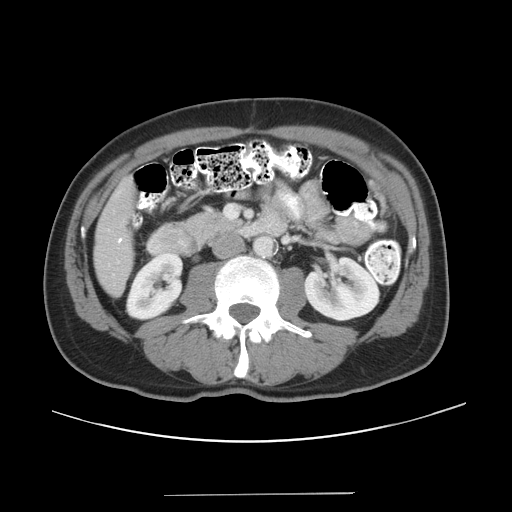
Contrast-enhanced abdominal CT, one axial slice; slice 11 of 43 in the series (ordered by position); 120 kVp; intravenous contrast given; soft-tissue window (W 400 / L 40 HU); 512 × 512 image matrix, field of view 409 × 409 mm. Male patient, age 65 years. From the clinical record (not read from this slice): diagnosis: colorectal cancer liver metastases, imaged before liver resection; multiple liver metastases: no; largest metastasis: 3.8 cm; disease in both lobes: no.
Outlined on this slice (expert manual segmentation):
- liver: bounding box <95,183,133,294> (left, top, right, bottom; pixels)
- planned liver remnant (the part of the liver to remain after resection): <95,183,133,294>